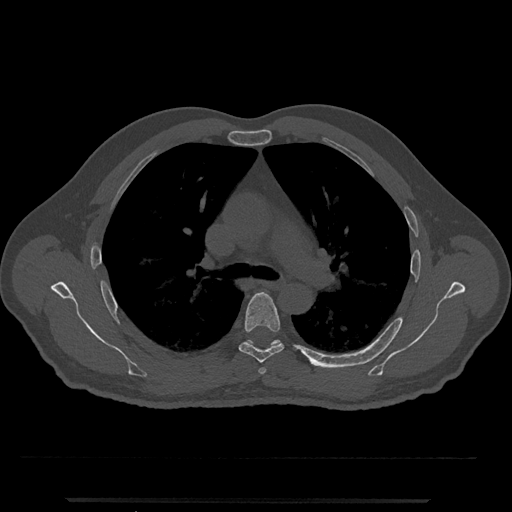
CT including the spine, one axial slice; position 786 of 797 along the scan axis; reconstruction kernel Br40s/3; bone window (W 1800 / L 400 HU); 0.5 mm slice thickness; 512 × 512 image matrix, field of view 419 × 419 mm. Male patient, age 63 years. From the clinical record (not read from this slice): primary cancer: prostate.
Annotated regions visible in this slice (semi-automatically segmented with operator editing):
- T5 vertebra: bounding box <239,292,284,363> (left, top, right, bottom; pixels)
- T6 vertebra: <246,340,281,347>